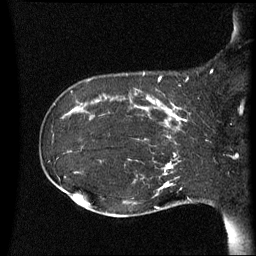
Breast MRI (dynamic contrast-enhanced), one sagittal slice. Dynamic contrast-enhanced series, image 2 of 3 at this slice position (ordered by acquisition). 1.5 T. TE 4.2 ms, TR 8.4 ms. 256 × 256 image matrix, field of view 220 × 220 mm. Patient: female, 41 years. From the clinical record (not read from this slice): setting: breast cancer imaged before/during neoadjuvant chemotherapy; receptor status: HER2-positive.
Outlined on this slice (semi-automatic segmentation, software-assisted and operator-edited):
- analysis volume of interest (the breast-tissue region the enhancement analysis was run in; not a lesion): bounding box [x1, y1, x2, y2] px = [122, 84, 195, 137]
- tumour enhancement mask (voxels above the 70 % enhancement threshold inside the analysis volume of interest): [136, 96, 186, 137]